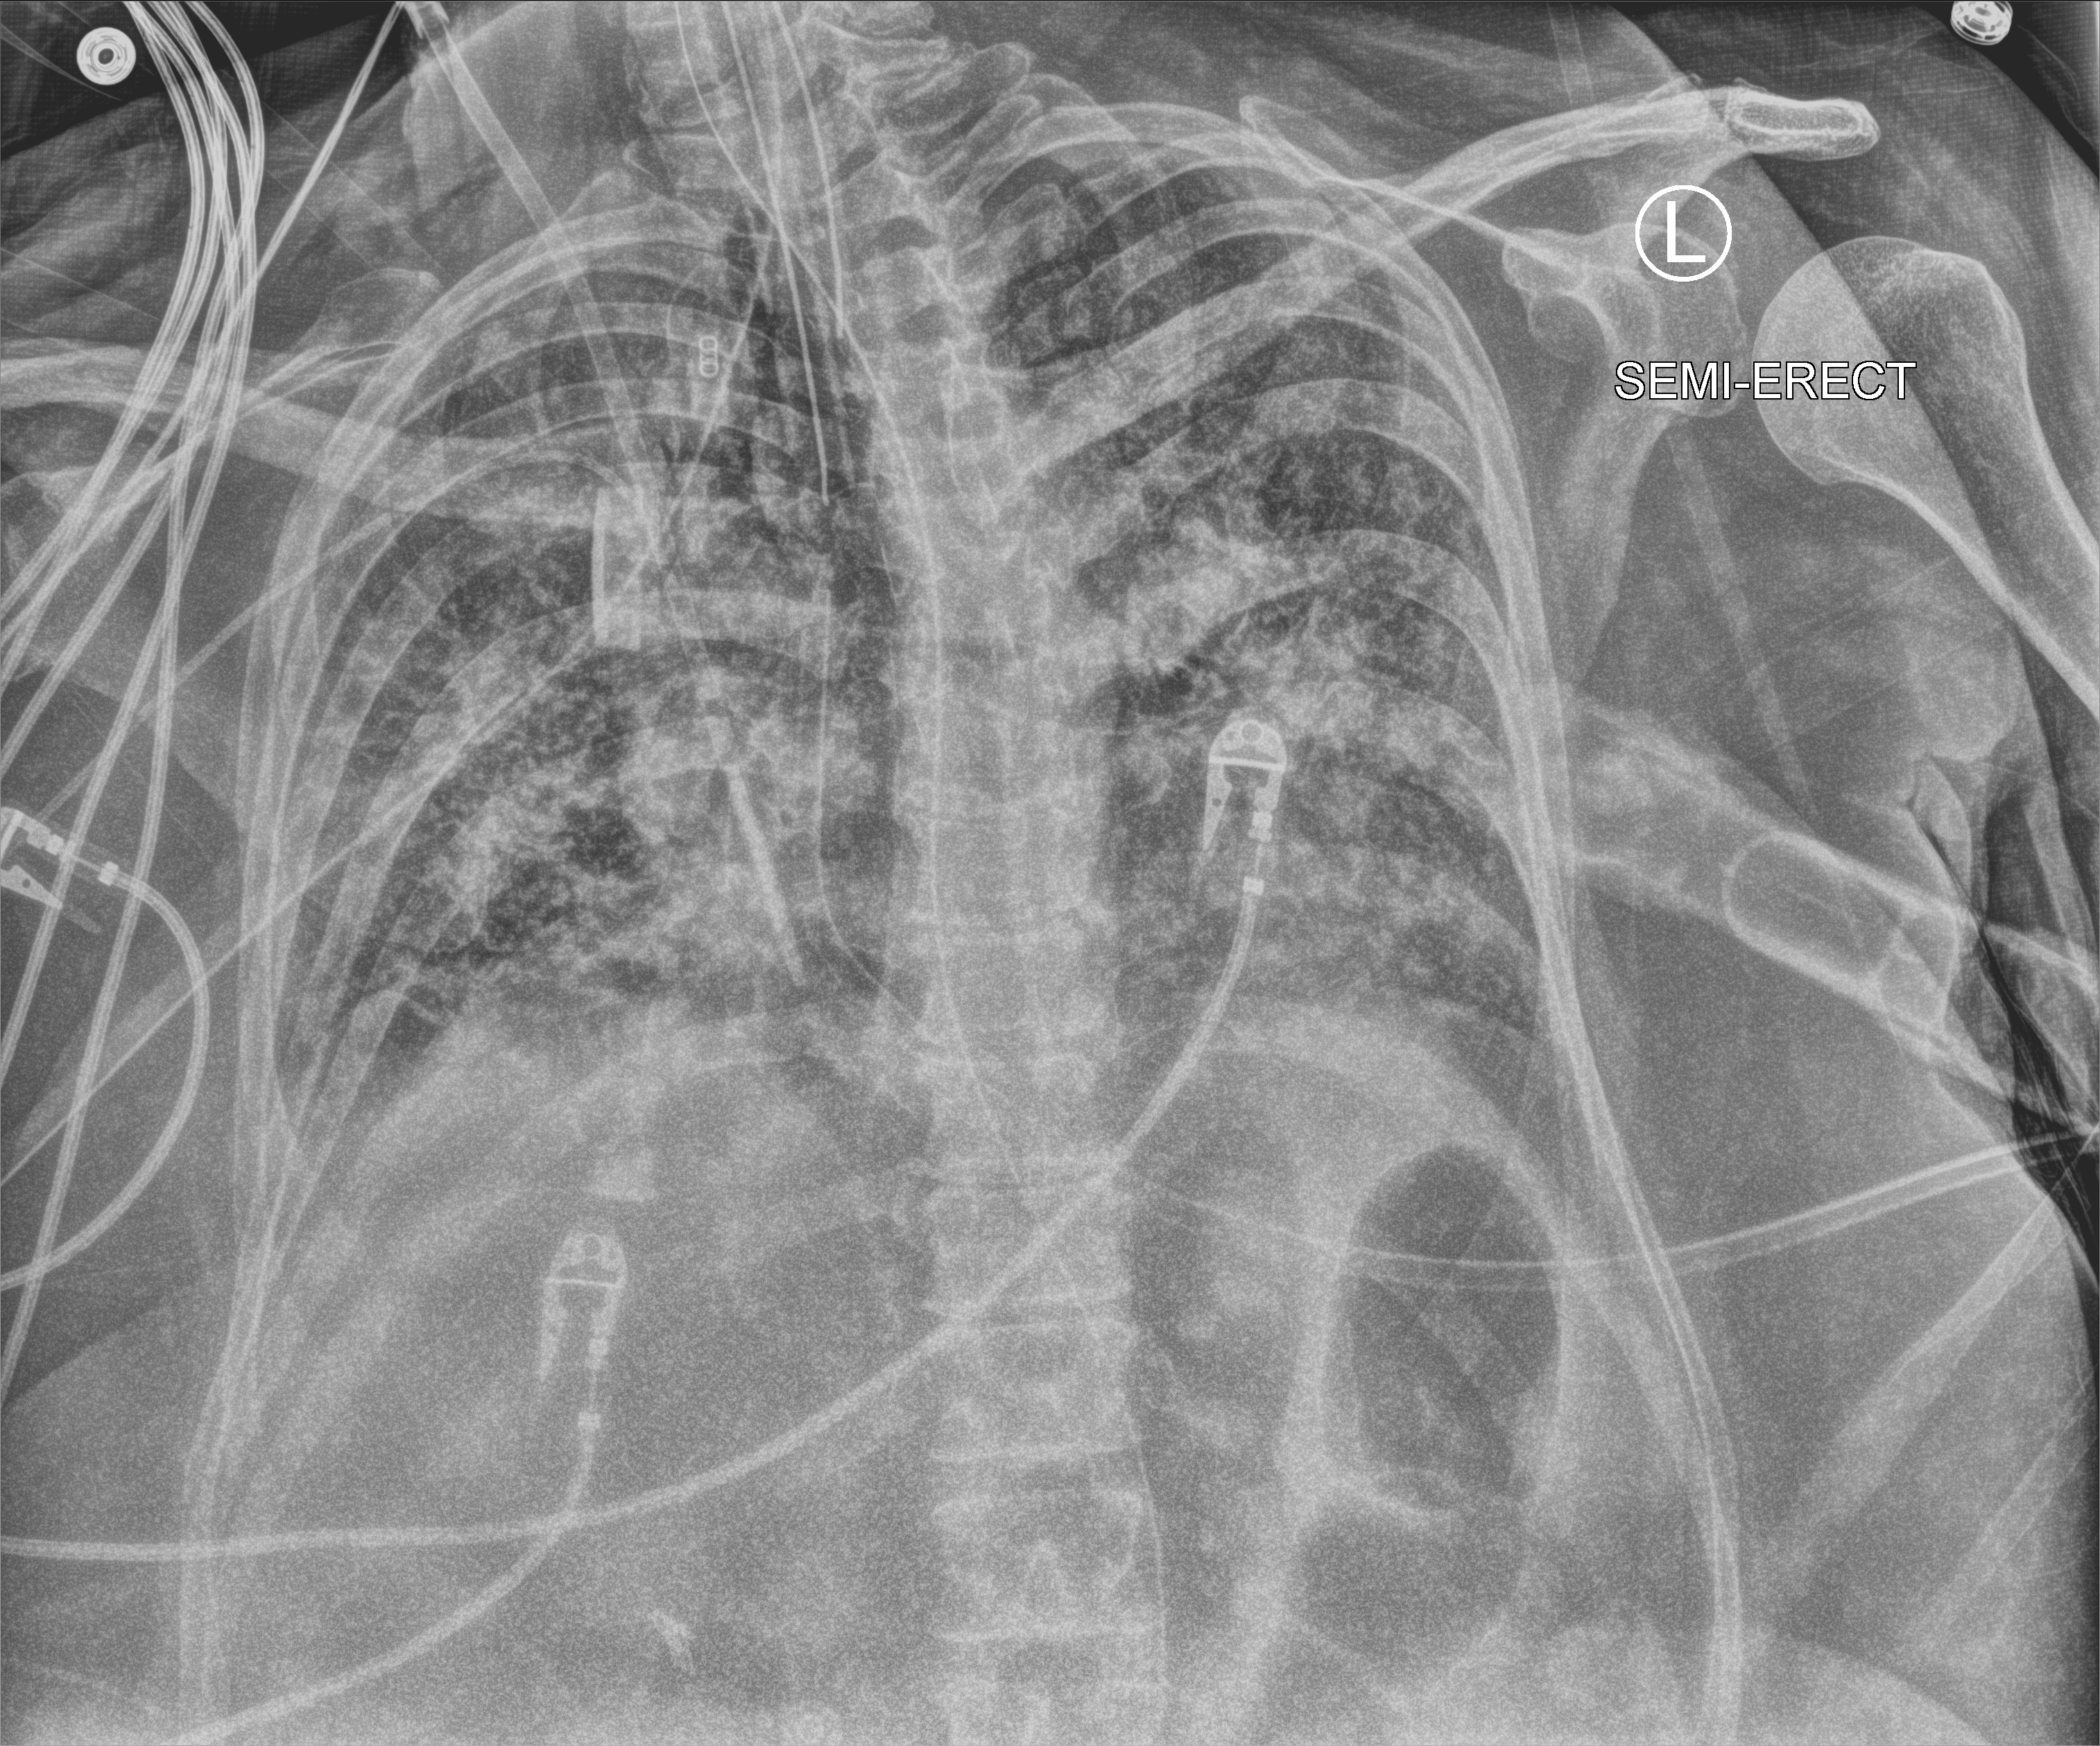
Portable chest radiograph; anteroposterior (AP) projection. Patient hospitalised with COVID-19; female, aged 60–74 years.
From the hospital-stay record, not from the radiograph (when in the stay this image was taken is not recorded): COPD (admission record): no; diabetes (admission record): no; hypertension (admission record): yes.